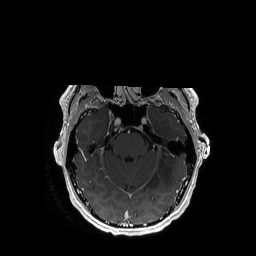
Brain MRI from a brain-tumour surgery series, one axial slice; position 121 of 192 along the scan axis; T1-weighted post-contrast; 1 mm slice thickness; 256 × 256 image matrix, field of view 256 × 256 mm. Case-level facts recorded for this patient, not image findings: histopathology: Astrocytoma; WHO grade: 3; IDH mutation: yes; tumour location: Left Temporal.
Outlined on this slice (expert manual segmentation):
- tumour: bounding box <149,123,178,187> (left, top, right, bottom; pixels)